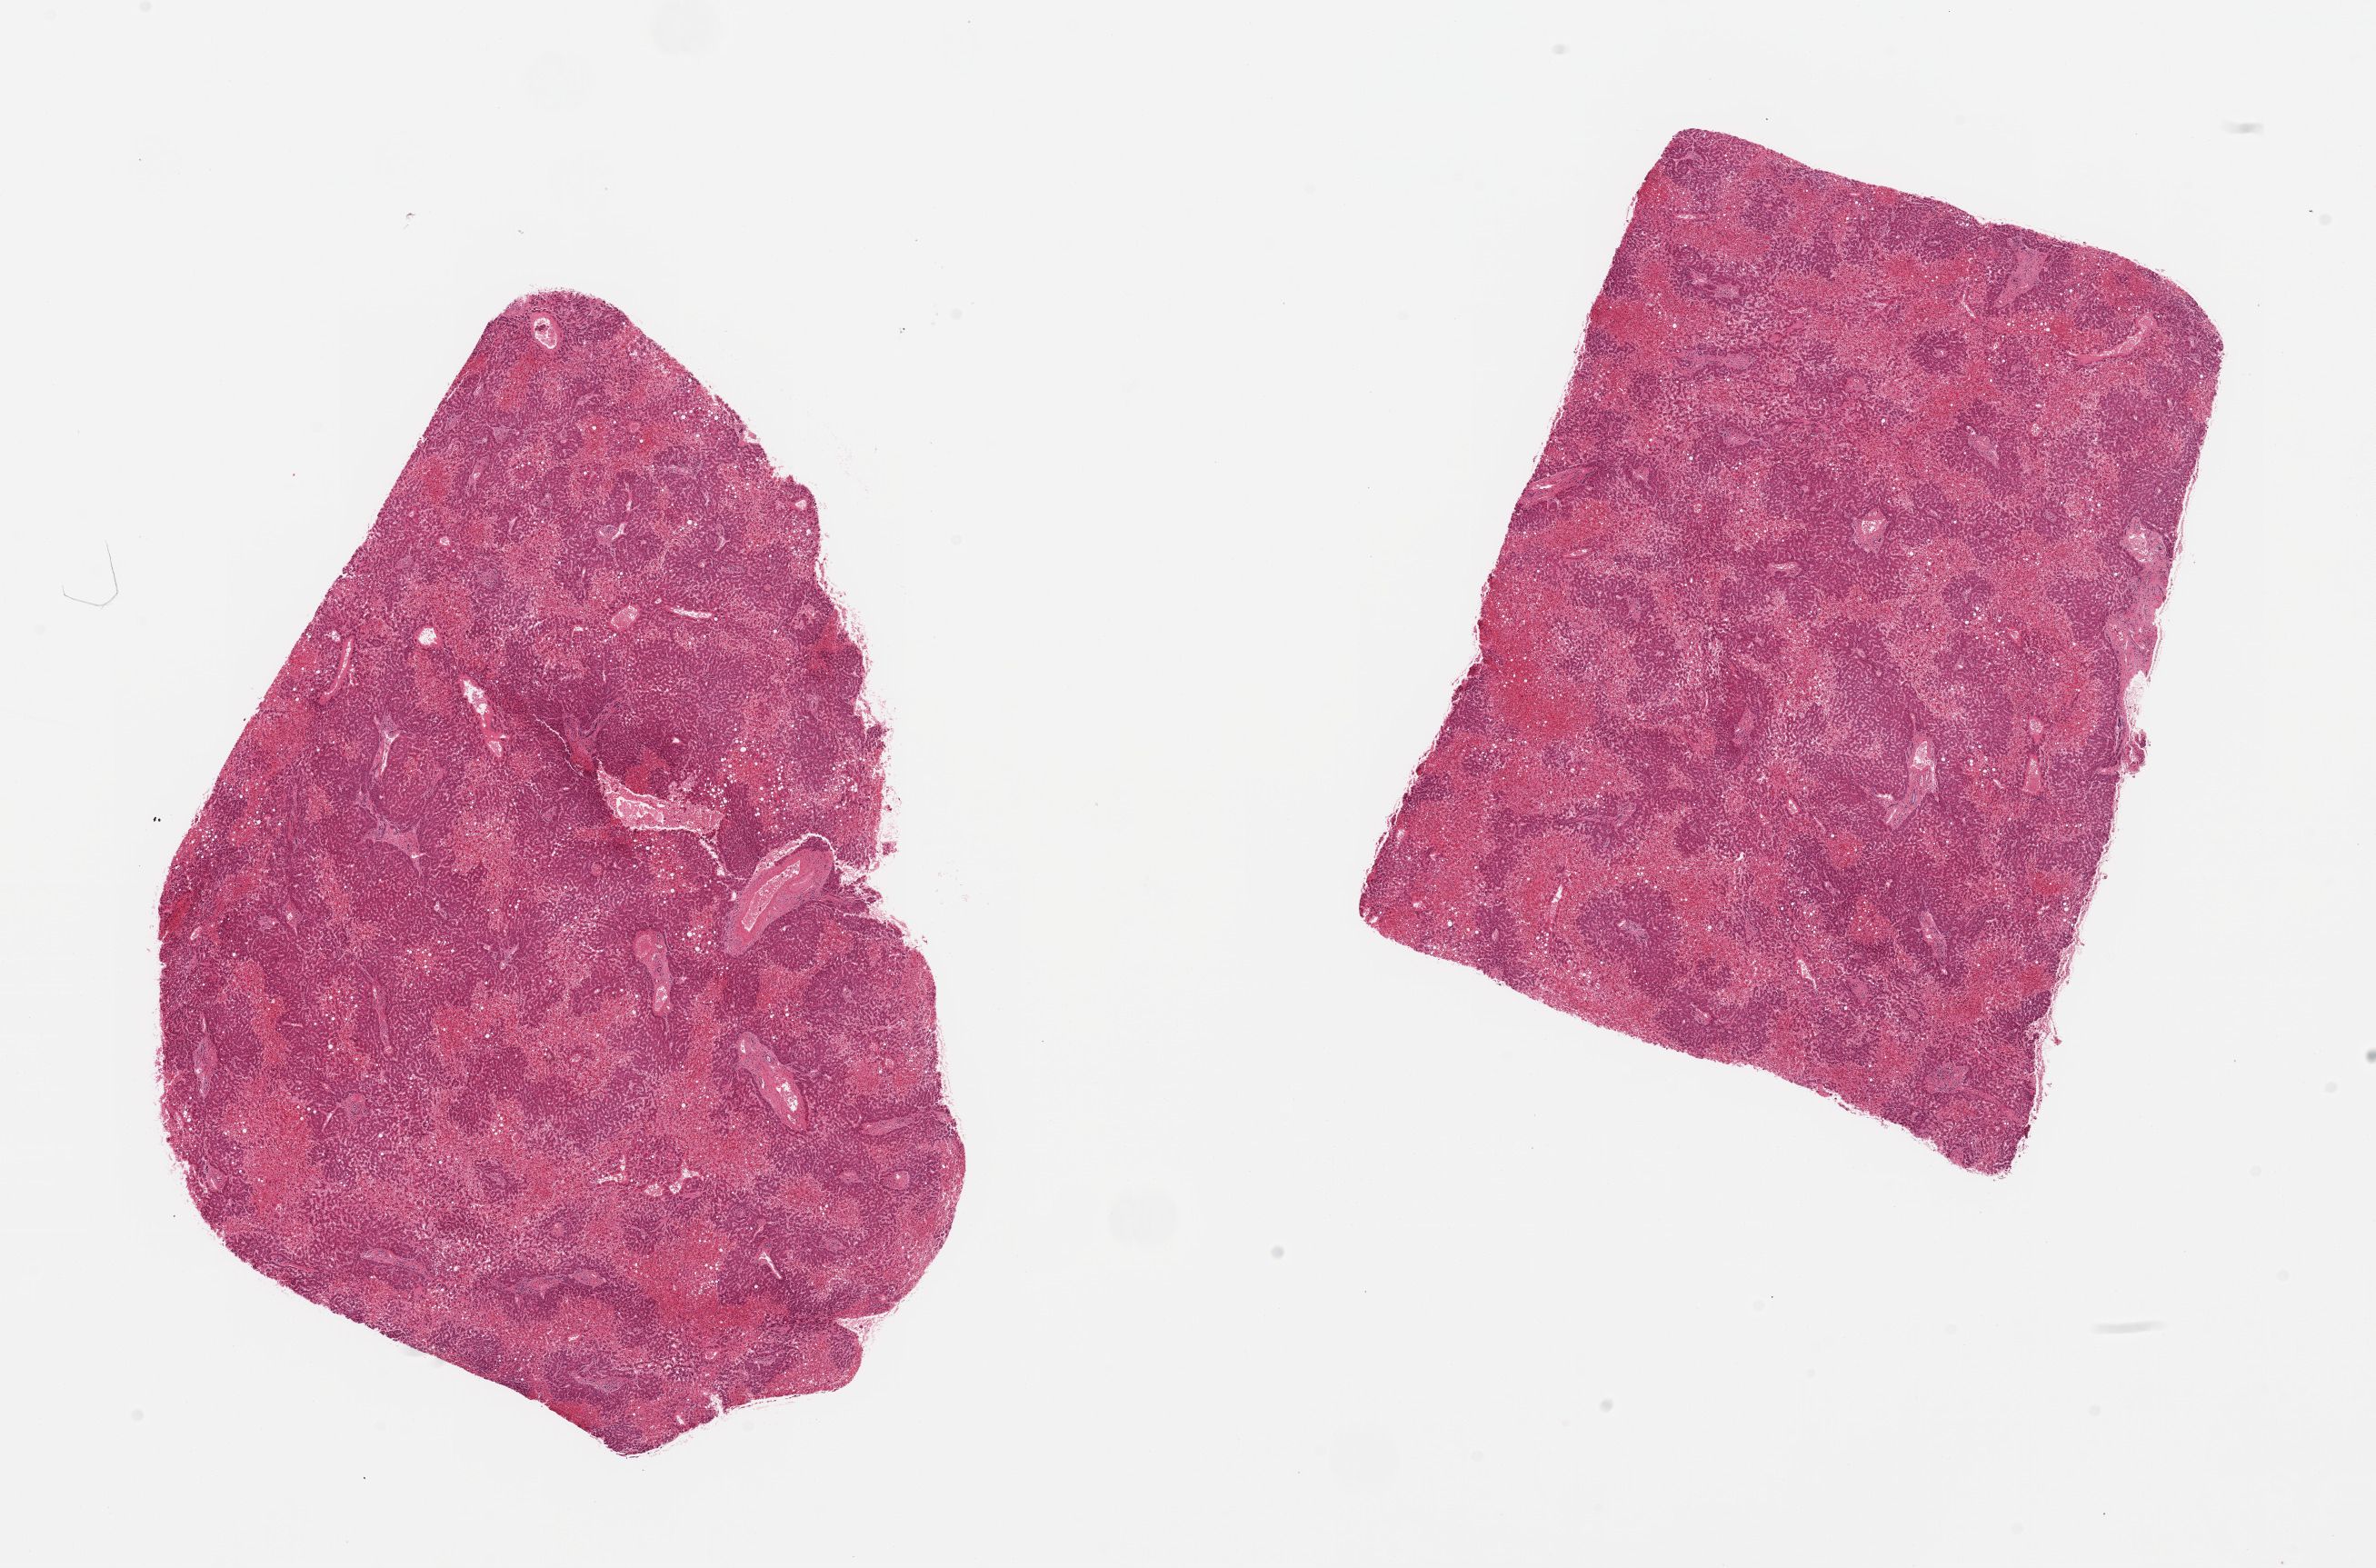
Whole-slide image, hematoxylin and eosin (H&E) stain, brightfield — shown as a low-resolution overview of the whole scanned area (about 20.7 x 13.6 mm, slide scanned at 20x); PAXgene-fixed, paraffin-embedded tissue; section of liver (target tissue); donor tissue sample. Male donor.
- reviewer comment on this tissue sample: 2 pieces; centrilobular necrosis, mild macrovesicular steatosis